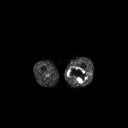
FDG PET of an extremity soft-tissue mass (from a PET/CT study), one axial slice. Slice 219 of 267 in the series (ordered by position). 3.27 mm slice thickness. 128 × 128 image matrix, field of view 700 × 700 mm. Male patient, age 44 years. Case-level facts recorded for this patient, not image findings: histological type: undifferentiated pleomorphic liposarcoma; grade: high; site of the primary tumour: left thigh.
Annotated regions visible in this slice (expert contour drawn on MRI and transferred to this co-registered scan by the dataset authors):
- gross tumour volume including surrounding oedema: bounding box [x1, y1, x2, y2] px = [68, 67, 87, 83]
- gross tumour volume (mass): [68, 67, 87, 83]